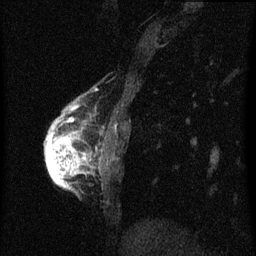
Breast MRI (dynamic contrast-enhanced), one sagittal slice. Slice 14 of 60 in the series (ordered by position). Dynamic contrast-enhanced series, image 2 of 3 at this slice position (ordered by acquisition). 1.5 T. TE 4.2 ms, TR 8 ms. 2 mm slice thickness. 256 × 256 image matrix, field of view 180 × 180 mm. Female patient, age 56 years.
Annotated regions visible in this slice (semi-automatic segmentation, software-assisted and operator-edited):
- analysis volume of interest (the breast-tissue region the enhancement analysis was run in; not a lesion): bounding box (x1, y1, x2, y2) in pixels: (46, 110, 89, 189)
- tumour enhancement mask (voxels above the 70 % enhancement threshold inside the analysis volume of interest): (46, 124, 85, 187)